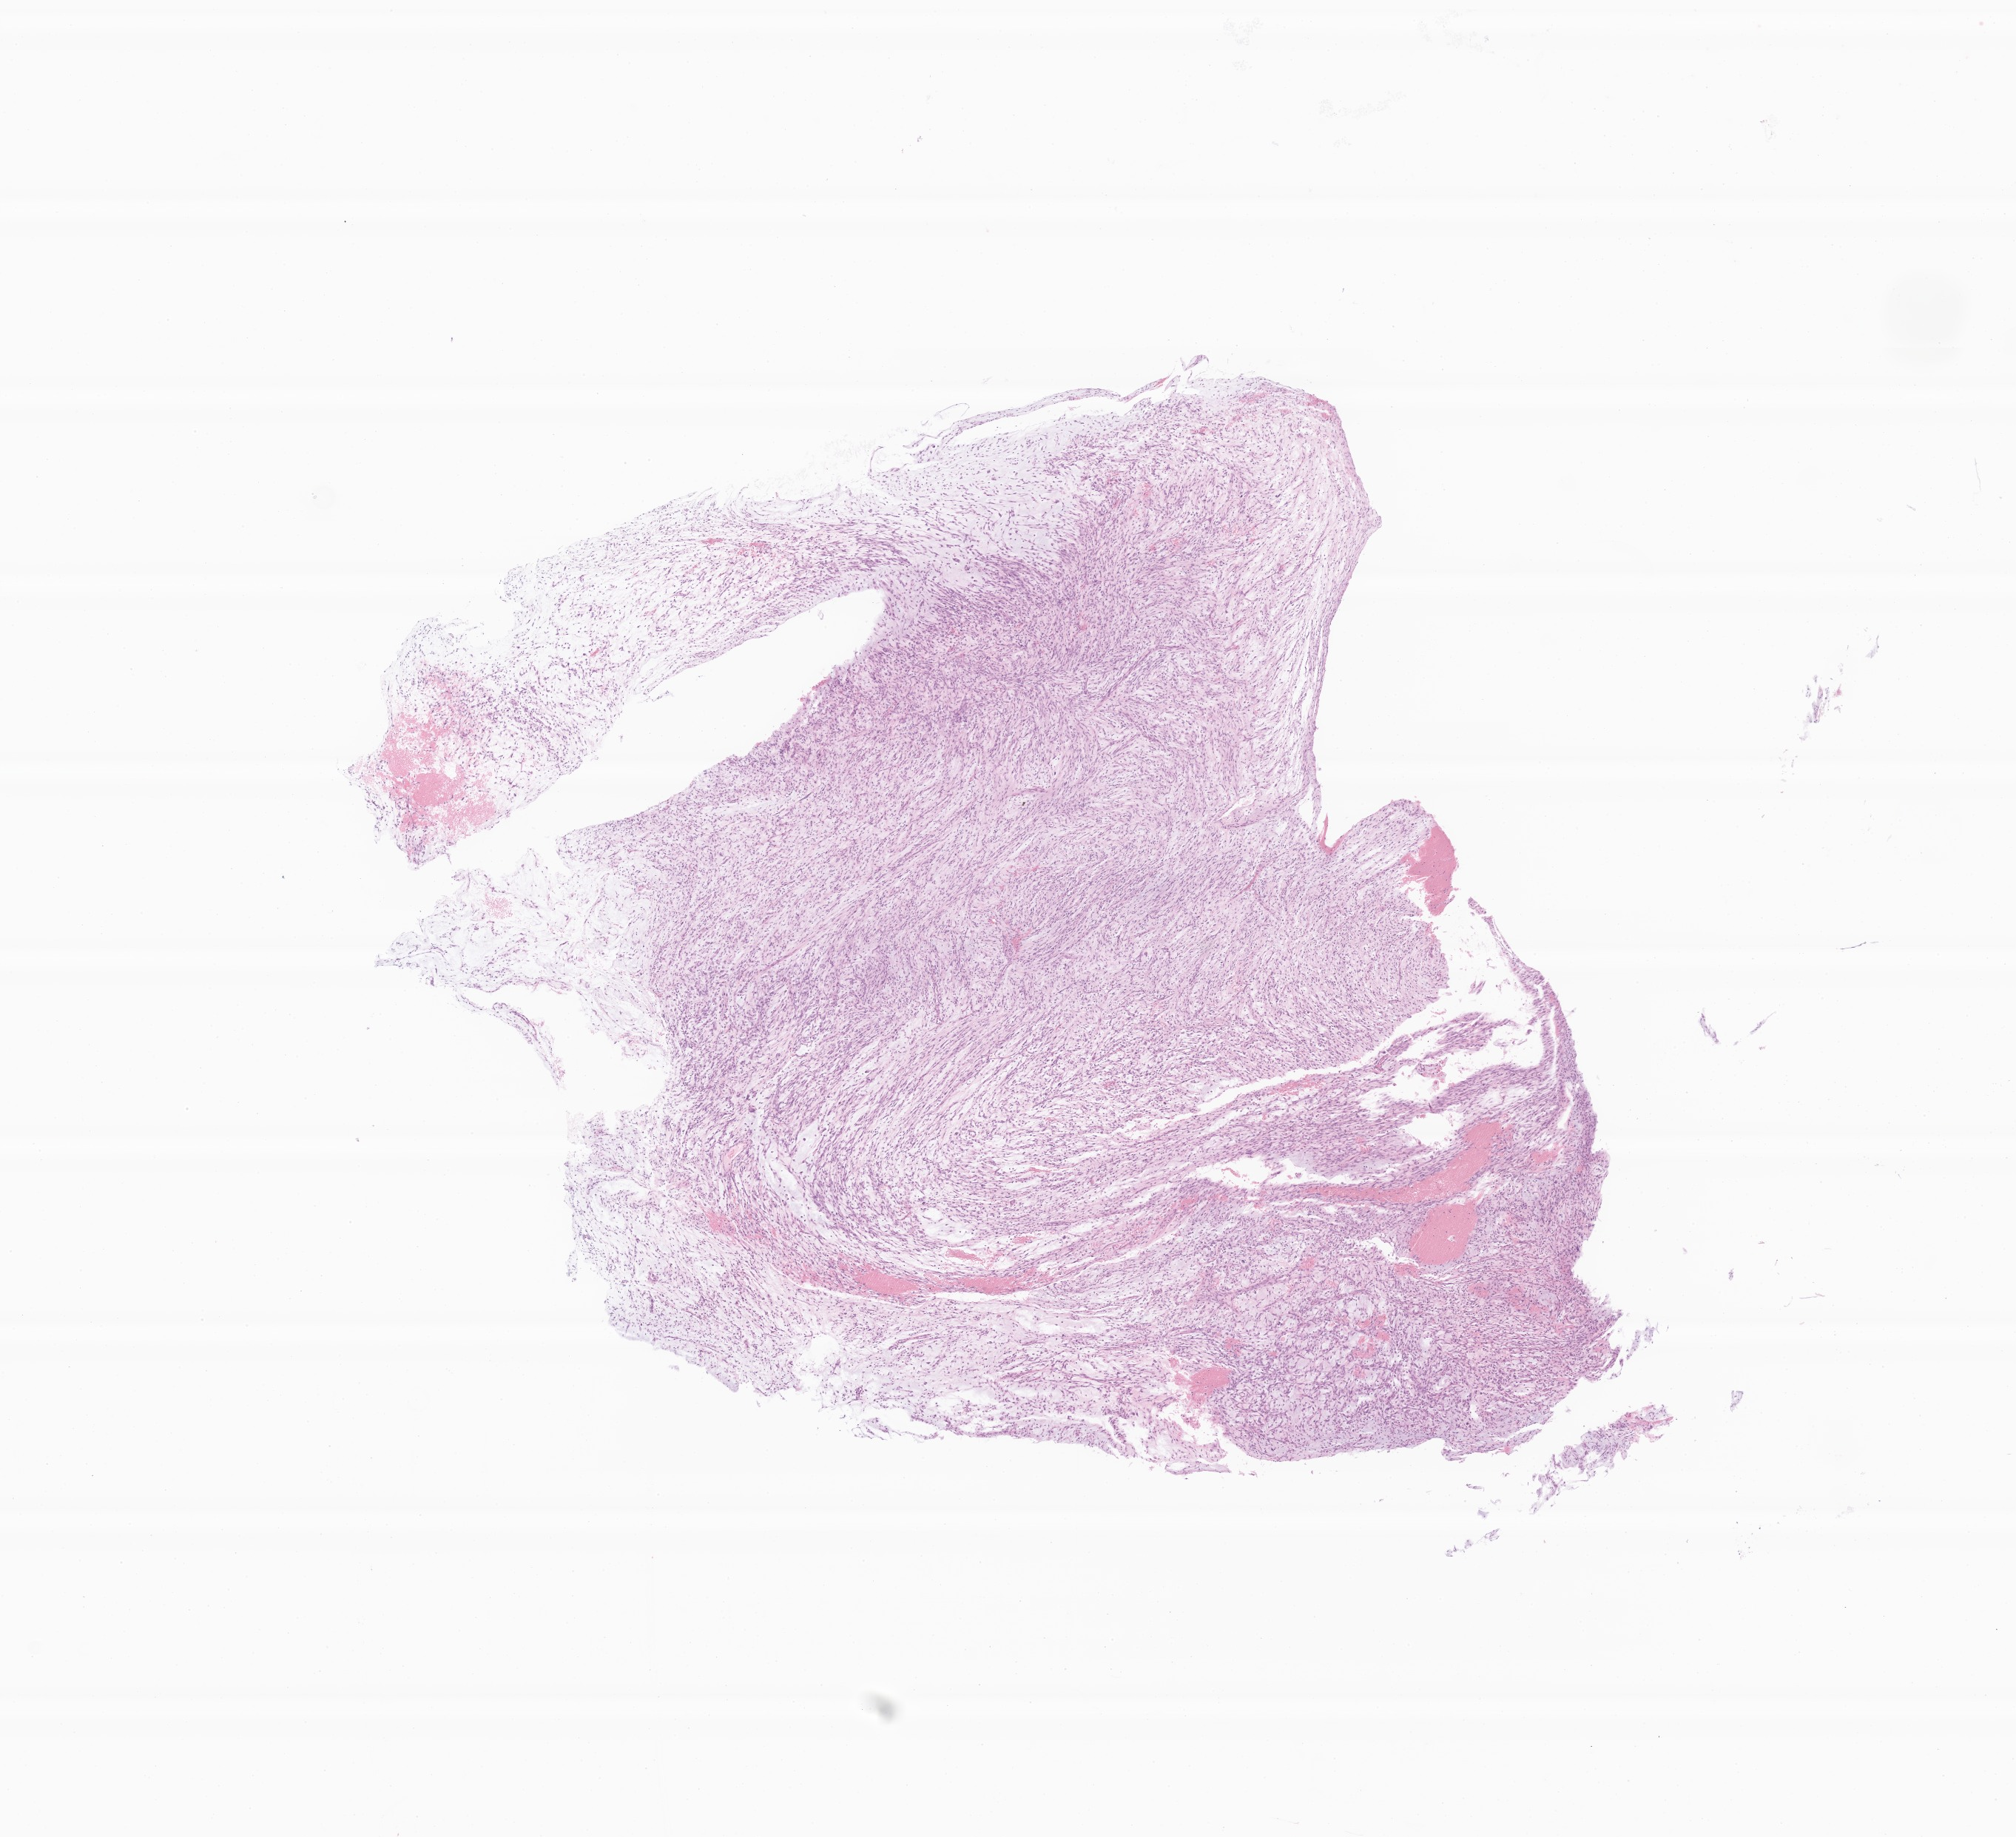
Haematoxylin and eosin whole-slide image of tumor tissue from the liver — whole scanned area (about 11.5 x 10.5 mm) shown as a low-resolution overview, FFPE section. Patient female; age 103 months.
- diagnosis (ICD-O-3 morphology term): Spindle cell sarcoma